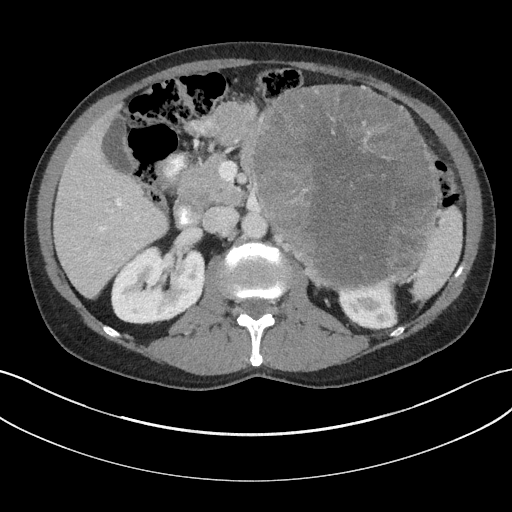
Contrast-enhanced abdominal CT, one axial slice; position 102 of 147 along the scan axis; 100 kVp; intravenous contrast given; soft-tissue window (W 400 / L 40 HU); 3 mm slice thickness; 512 × 512 image matrix, field of view 384 × 384 mm. Male patient, age 58 years. Case-level facts recorded for this patient, not image findings: diagnosis: adrenocortical carcinoma; tumour side: left adrenal; tumour size at pathology: 22 cm; Ki-67 index: 26 %; stage (as recorded): 2.
Annotated regions visible in this slice (semi-automatic segmentation, software-assisted and operator-edited):
- mass: box from (x=255, y=86) to (x=436, y=285) px